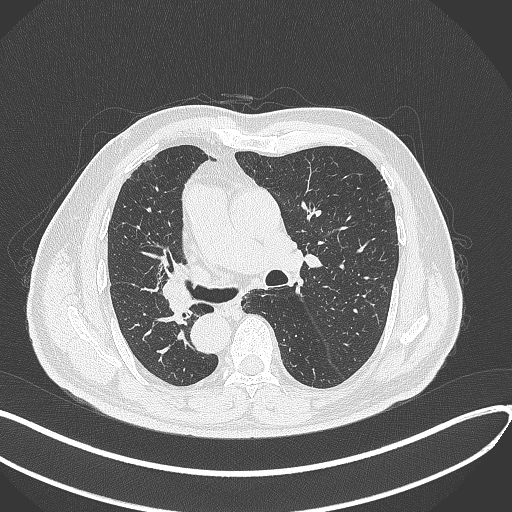
Chest CT, one axial slice. Position 166 of 300 along the scan axis. Reconstruction kernel B70f. 120 kVp. Lung window (W 1500 / L -600 HU). 1 mm slice thickness. 512 × 512 image matrix, field of view 400 × 400 mm. Patient: male, 67 years. Case-level facts recorded for this patient, not image findings: clinical TNM (as recorded): T2a N0 M0.
Structures marked on this image (rectangle marked by the reading radiologist):
- lung tumour (recorded histology: squamous cell carcinoma): bounding box (x1, y1, x2, y2) in pixels: (157, 277, 193, 322)